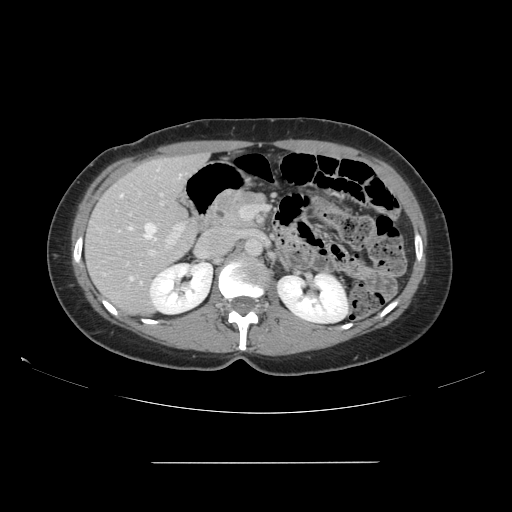
Contrast-enhanced abdominal CT, one axial slice. Slice 84 of 151 in the series (ordered by position). 120 kVp. Soft-tissue window (W 400 / L 40 HU). 2.5 mm slice thickness. 512 × 512 image matrix. Female patient, age 46 years. Case-level facts recorded for this patient, not image findings: diagnosis: colorectal cancer liver metastases, imaged before liver resection; multiple liver metastases: yes; largest metastasis: 3 cm; disease in both lobes: yes.
Outlined on this slice (expert manual segmentation):
- hepatic veins: box from (x=119, y=175) to (x=181, y=279) px
- liver: (x=86, y=155)–(x=207, y=315)
- planned liver remnant (the part of the liver to remain after resection): (x=95, y=155)–(x=202, y=313)
- portal vein (with intrahepatic branches): (x=129, y=191)–(x=247, y=258)